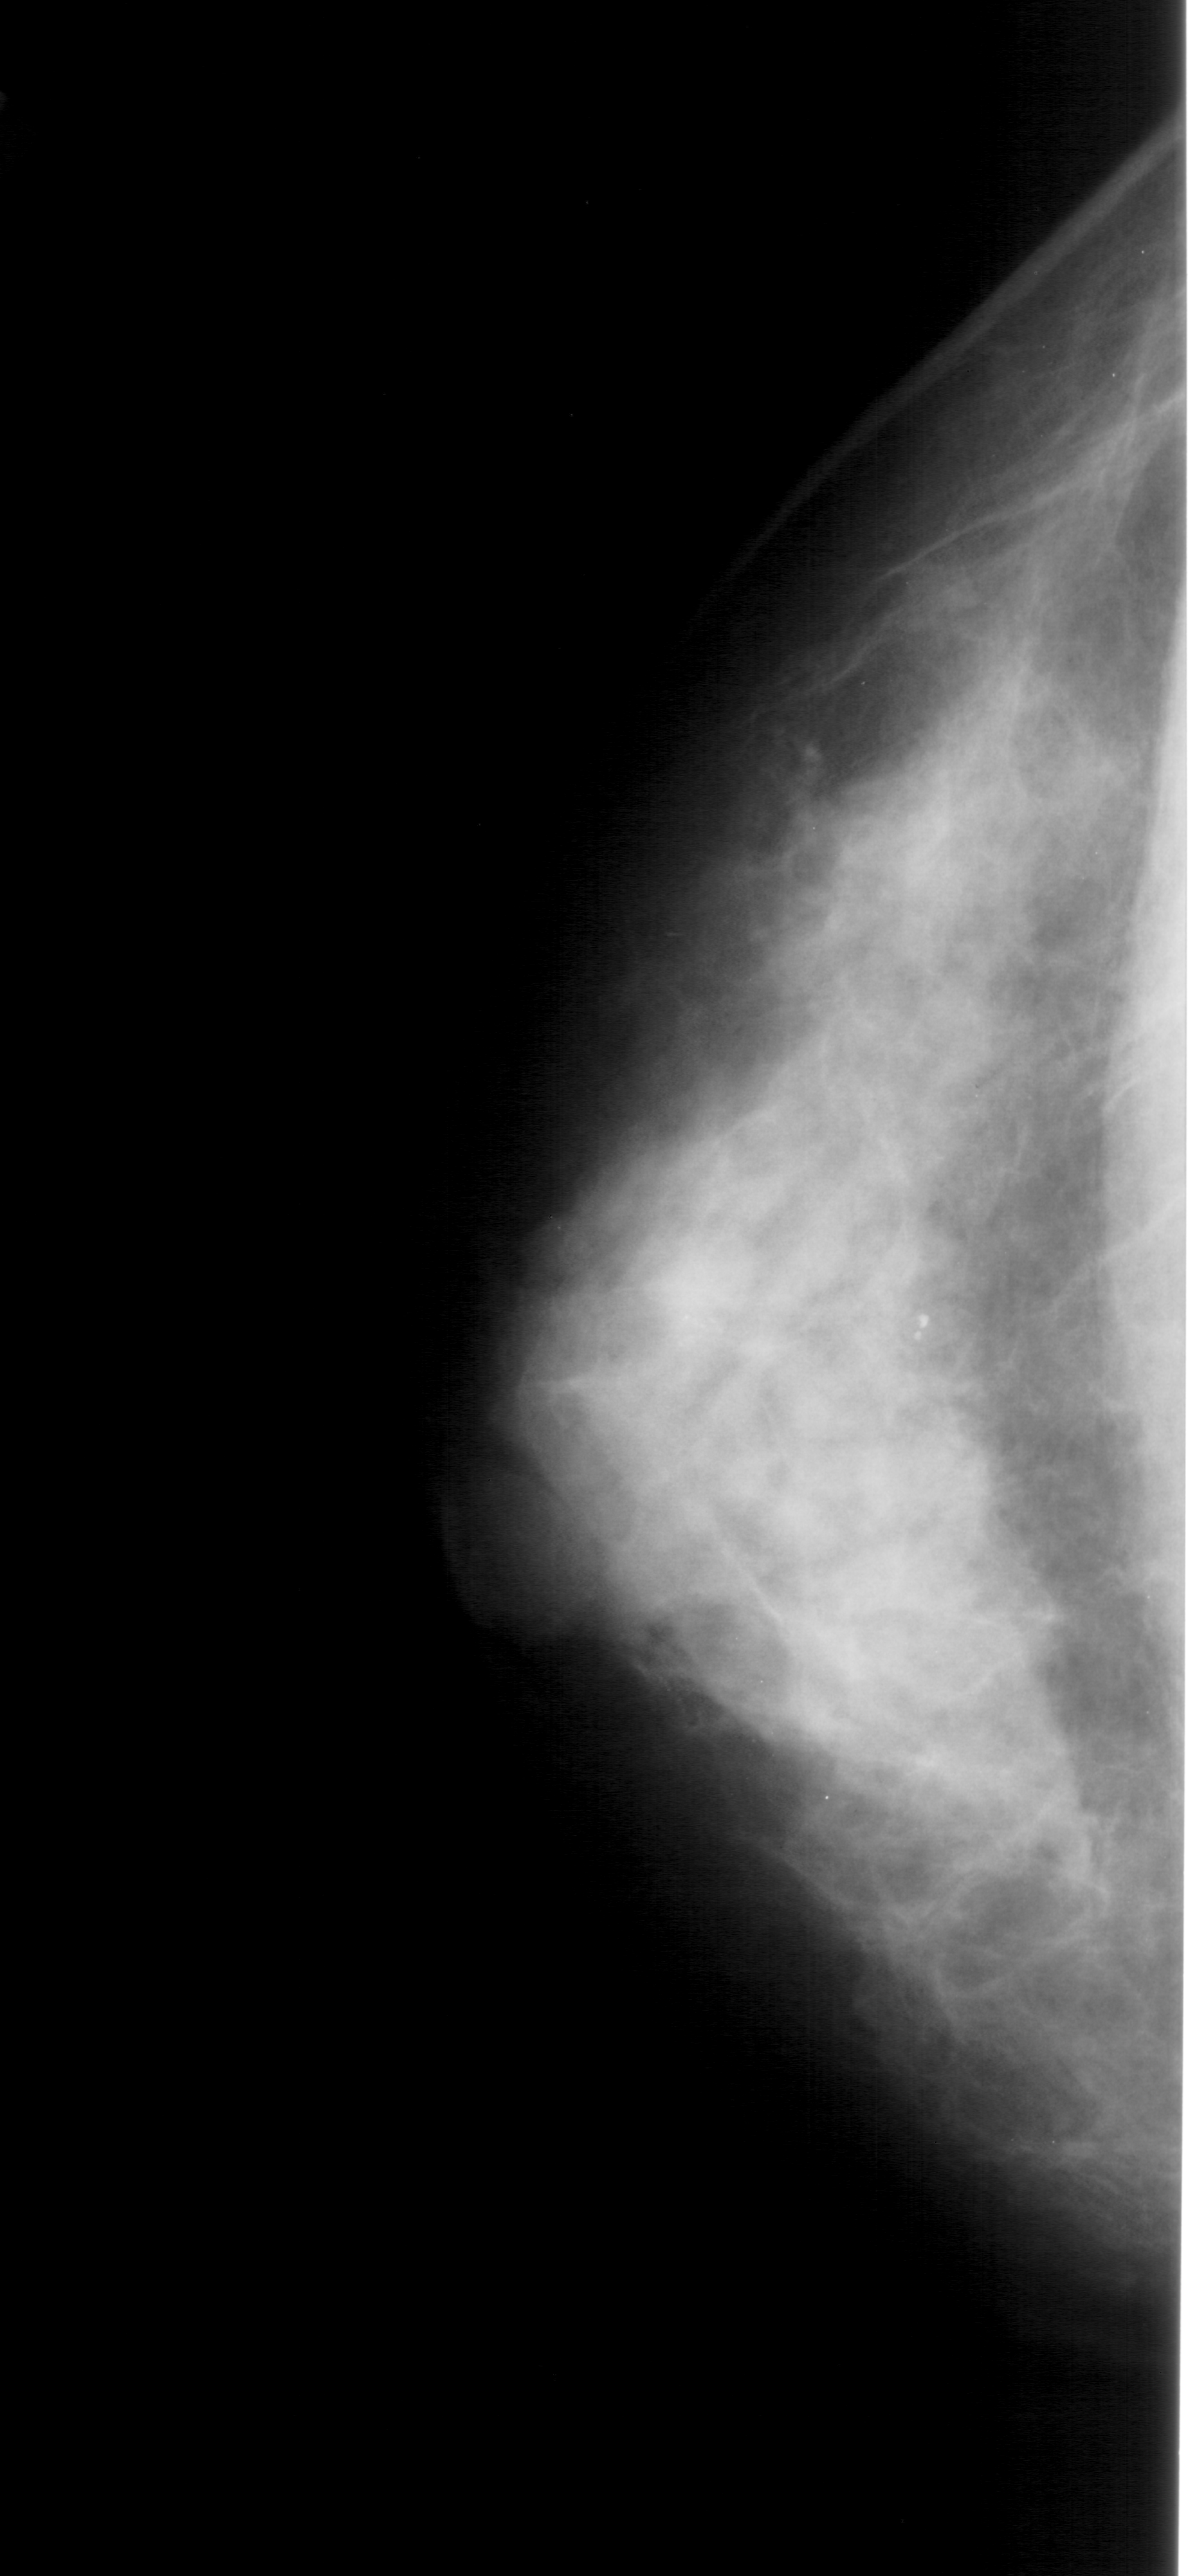
Scanned film-screen mammogram; left breast; CC view.
Radiologist-marked abnormalities on this image: calcifications, morphology pleomorphic, distribution clustered; BI-RADS assessment category 4; subtlety rating 2 on a 1 (subtle) to 5 (obvious) scale; pathology result (as recorded, not read from the image): benign.